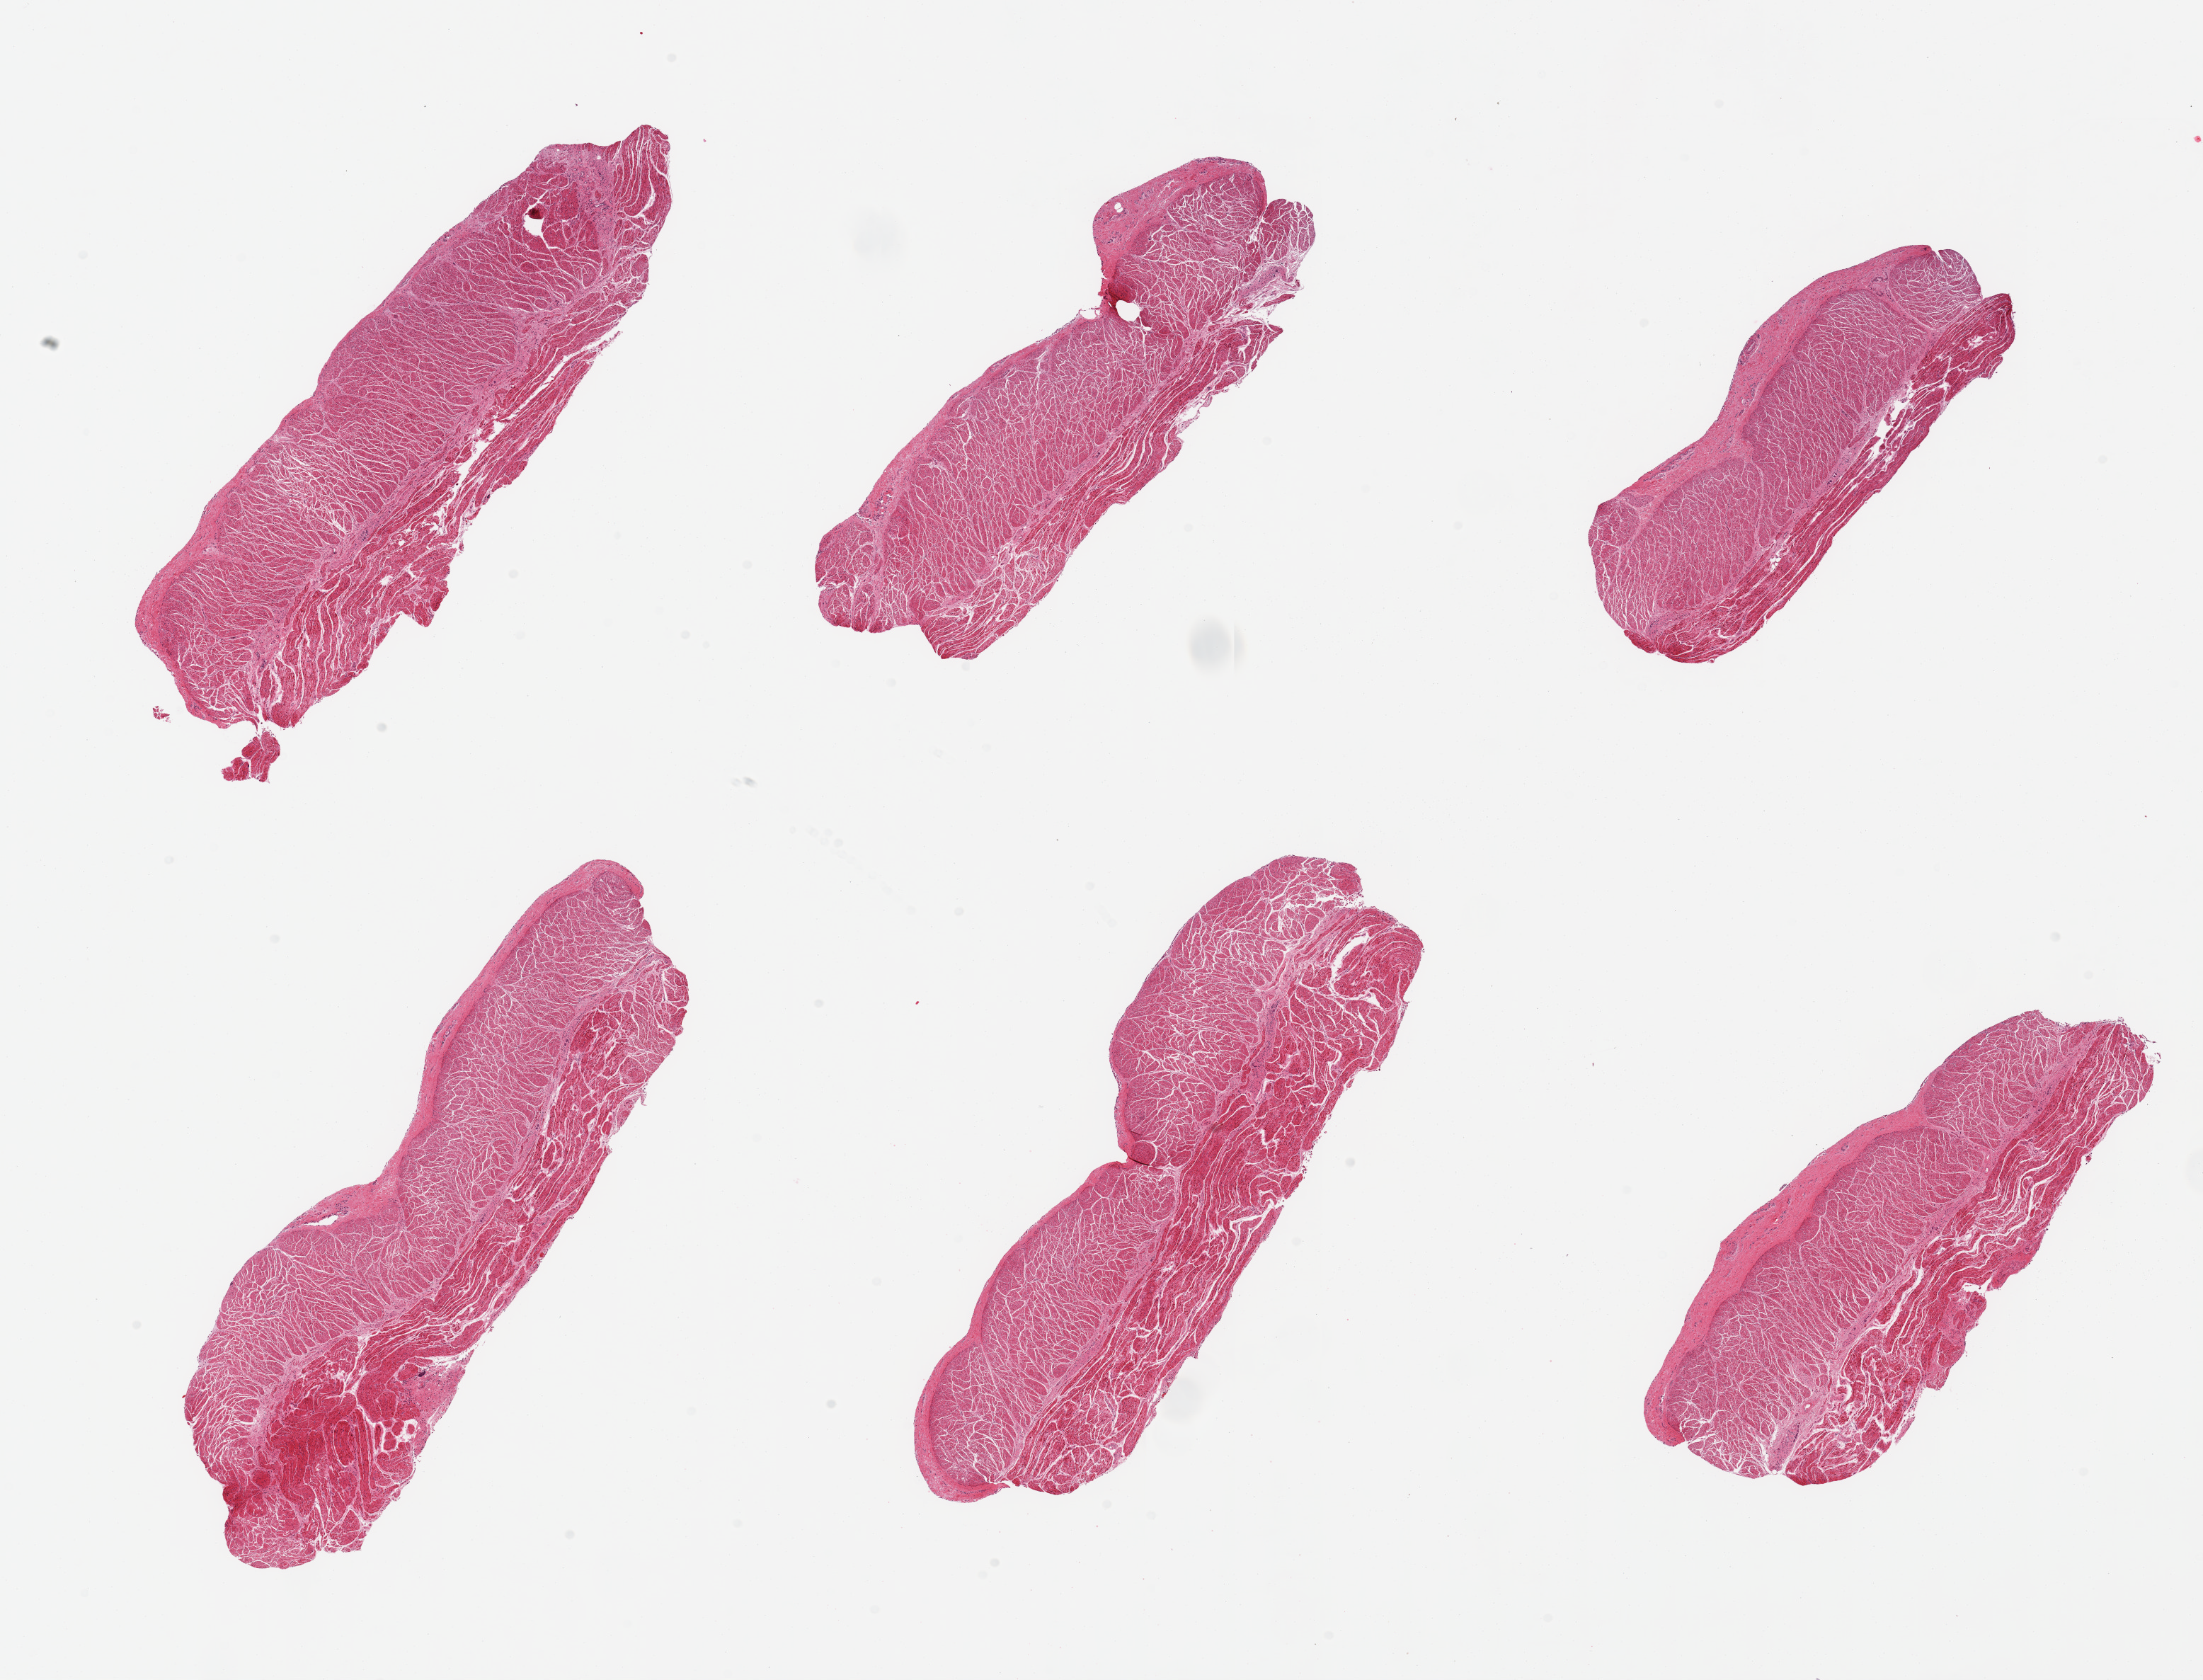
Digitized haematoxylin and eosin-stained section, whole scanned area (about 24.6 x 18.8 mm) shown as a low-resolution overview. PAXgene-fixed paraffin-embedded (PFPE) section. Section of esophageal muscle (target tissue). Tissue donor sample.
Reviewer comment on this tissue sample: 6 pieces; well trimmed muscle.